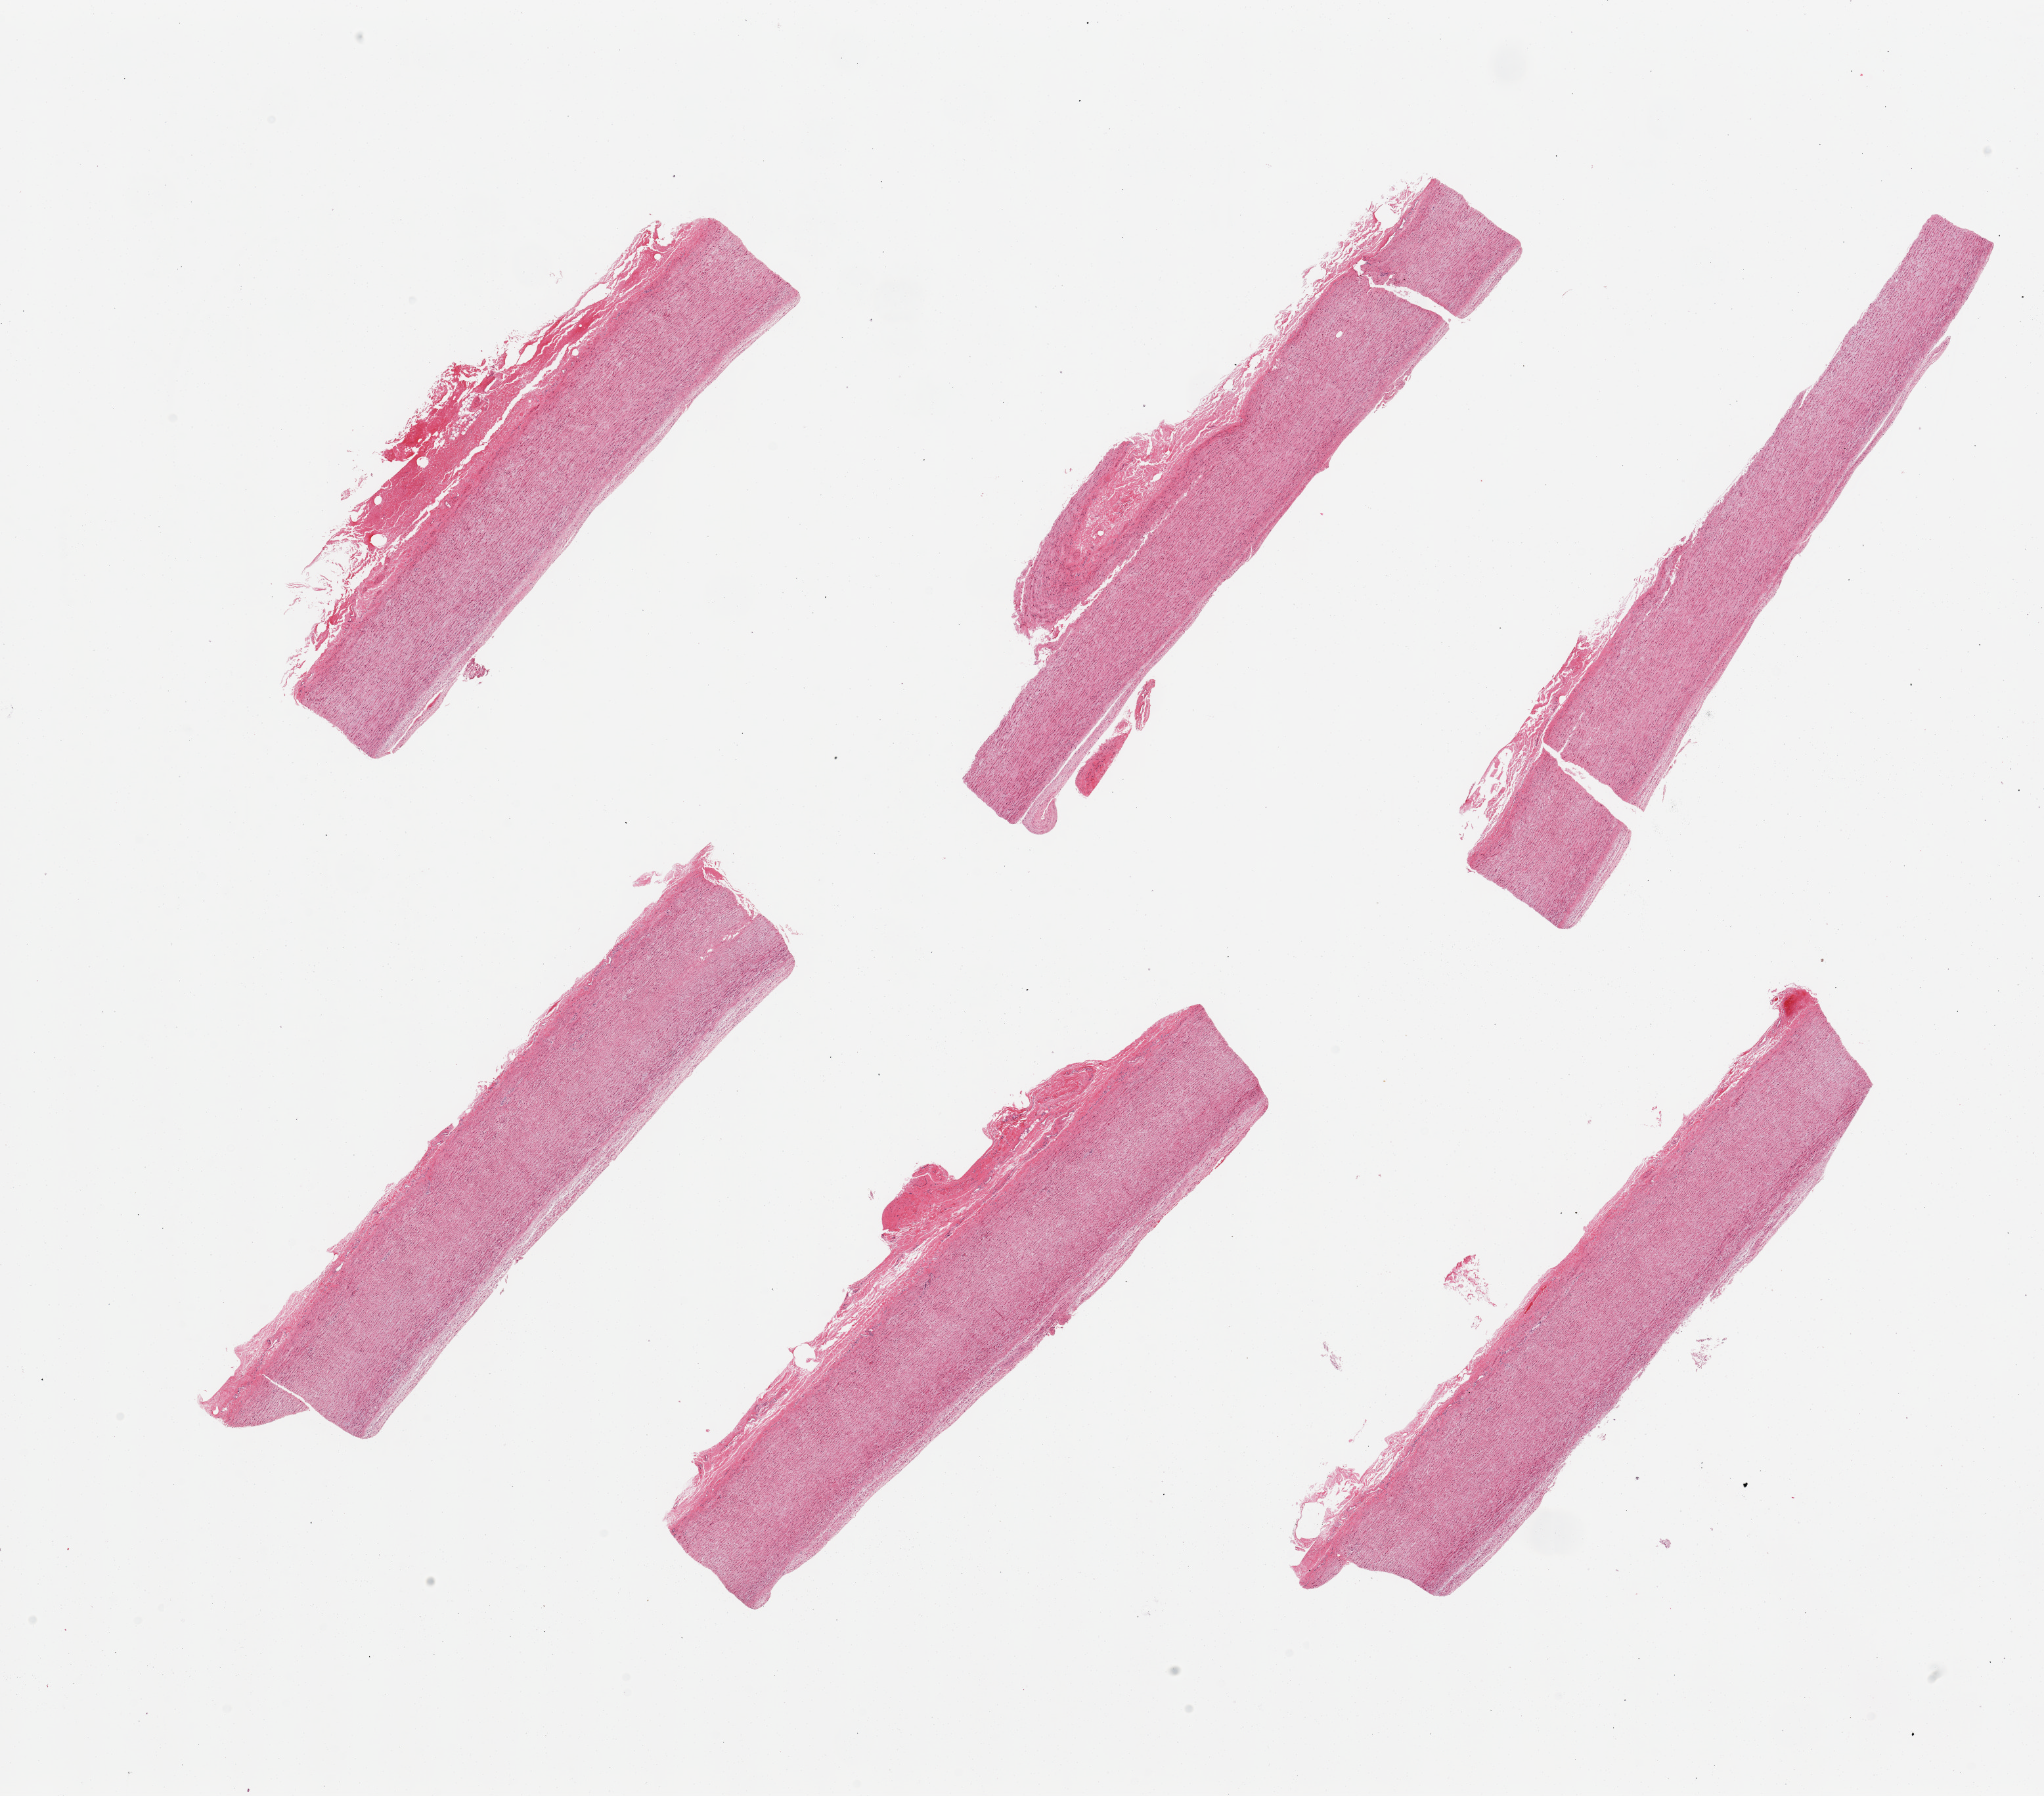
Haematoxylin and eosin whole-slide image — a low-resolution overview of the entire scanned area, about 24.6 x 21.6 mm (acquisition: 20x scan). PAXgene-fixed, paraffin-embedded tissue. Section of aorta (target tissue). Donor tissue sample. Donor sex: male.
Pathologist's review note for this sample: 6 pieces, minimal atherosis.